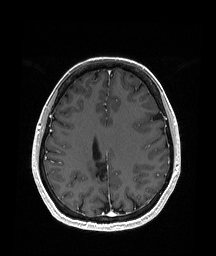
Brain MRI from a brain-tumour surgery series, one axial slice. Position 72 of 151 along the scan axis. T1-weighted post-contrast. 1.05 mm slice thickness. 216 × 256 image matrix, field of view 211 × 250 mm. Case-level facts recorded for this patient, not image findings: histopathology: Oligodendroglioma; WHO grade: 2; IDH mutation: yes; tumour location: Right Parietal.
Annotated regions visible in this slice (expert manual segmentation):
- previous resection cavity: bounding box [x1, y1, x2, y2] px = [94, 156, 109, 175]